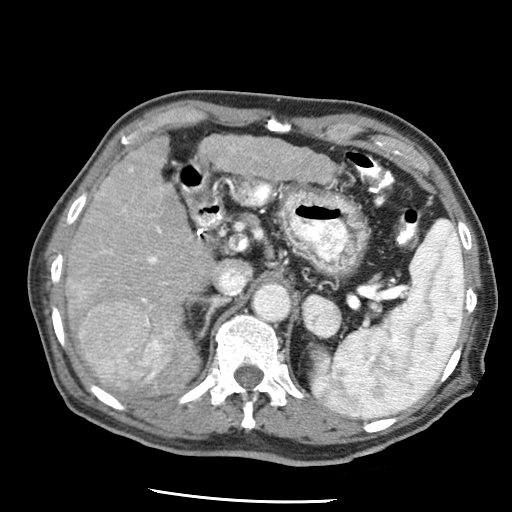
Contrast-enhanced abdominal CT (liver protocol), one axial slice; slice 32 of 79 in the series (ordered by position); reconstruction kernel STANDARD; 120 kVp; soft-tissue window (W 400 / L 40 HU); 2.5 mm slice thickness; 512 × 512 image matrix, field of view 320 × 320 mm. Case-level facts recorded for this patient, not image findings: diagnosis: hepatocellular carcinoma (patient treated with transarterial chemoembolisation; whether this scan precedes or follows treatment is not stated here); TNM stage (as recorded): Stage-IIIA; Child-Pugh class: A; tumour differentiation: moderately differentiated; tumour nodularity: multinodular.
Structures marked on this image (semi-automatically segmented with operator editing):
- liver parenchyma outside the tumour (the mass and vessels are separate outlines, so this box may not span the whole liver): box from (x=66, y=138) to (x=214, y=392) px
- mass: (x=66, y=279)–(x=169, y=389)
- liver vessels: (x=101, y=168)–(x=173, y=382)